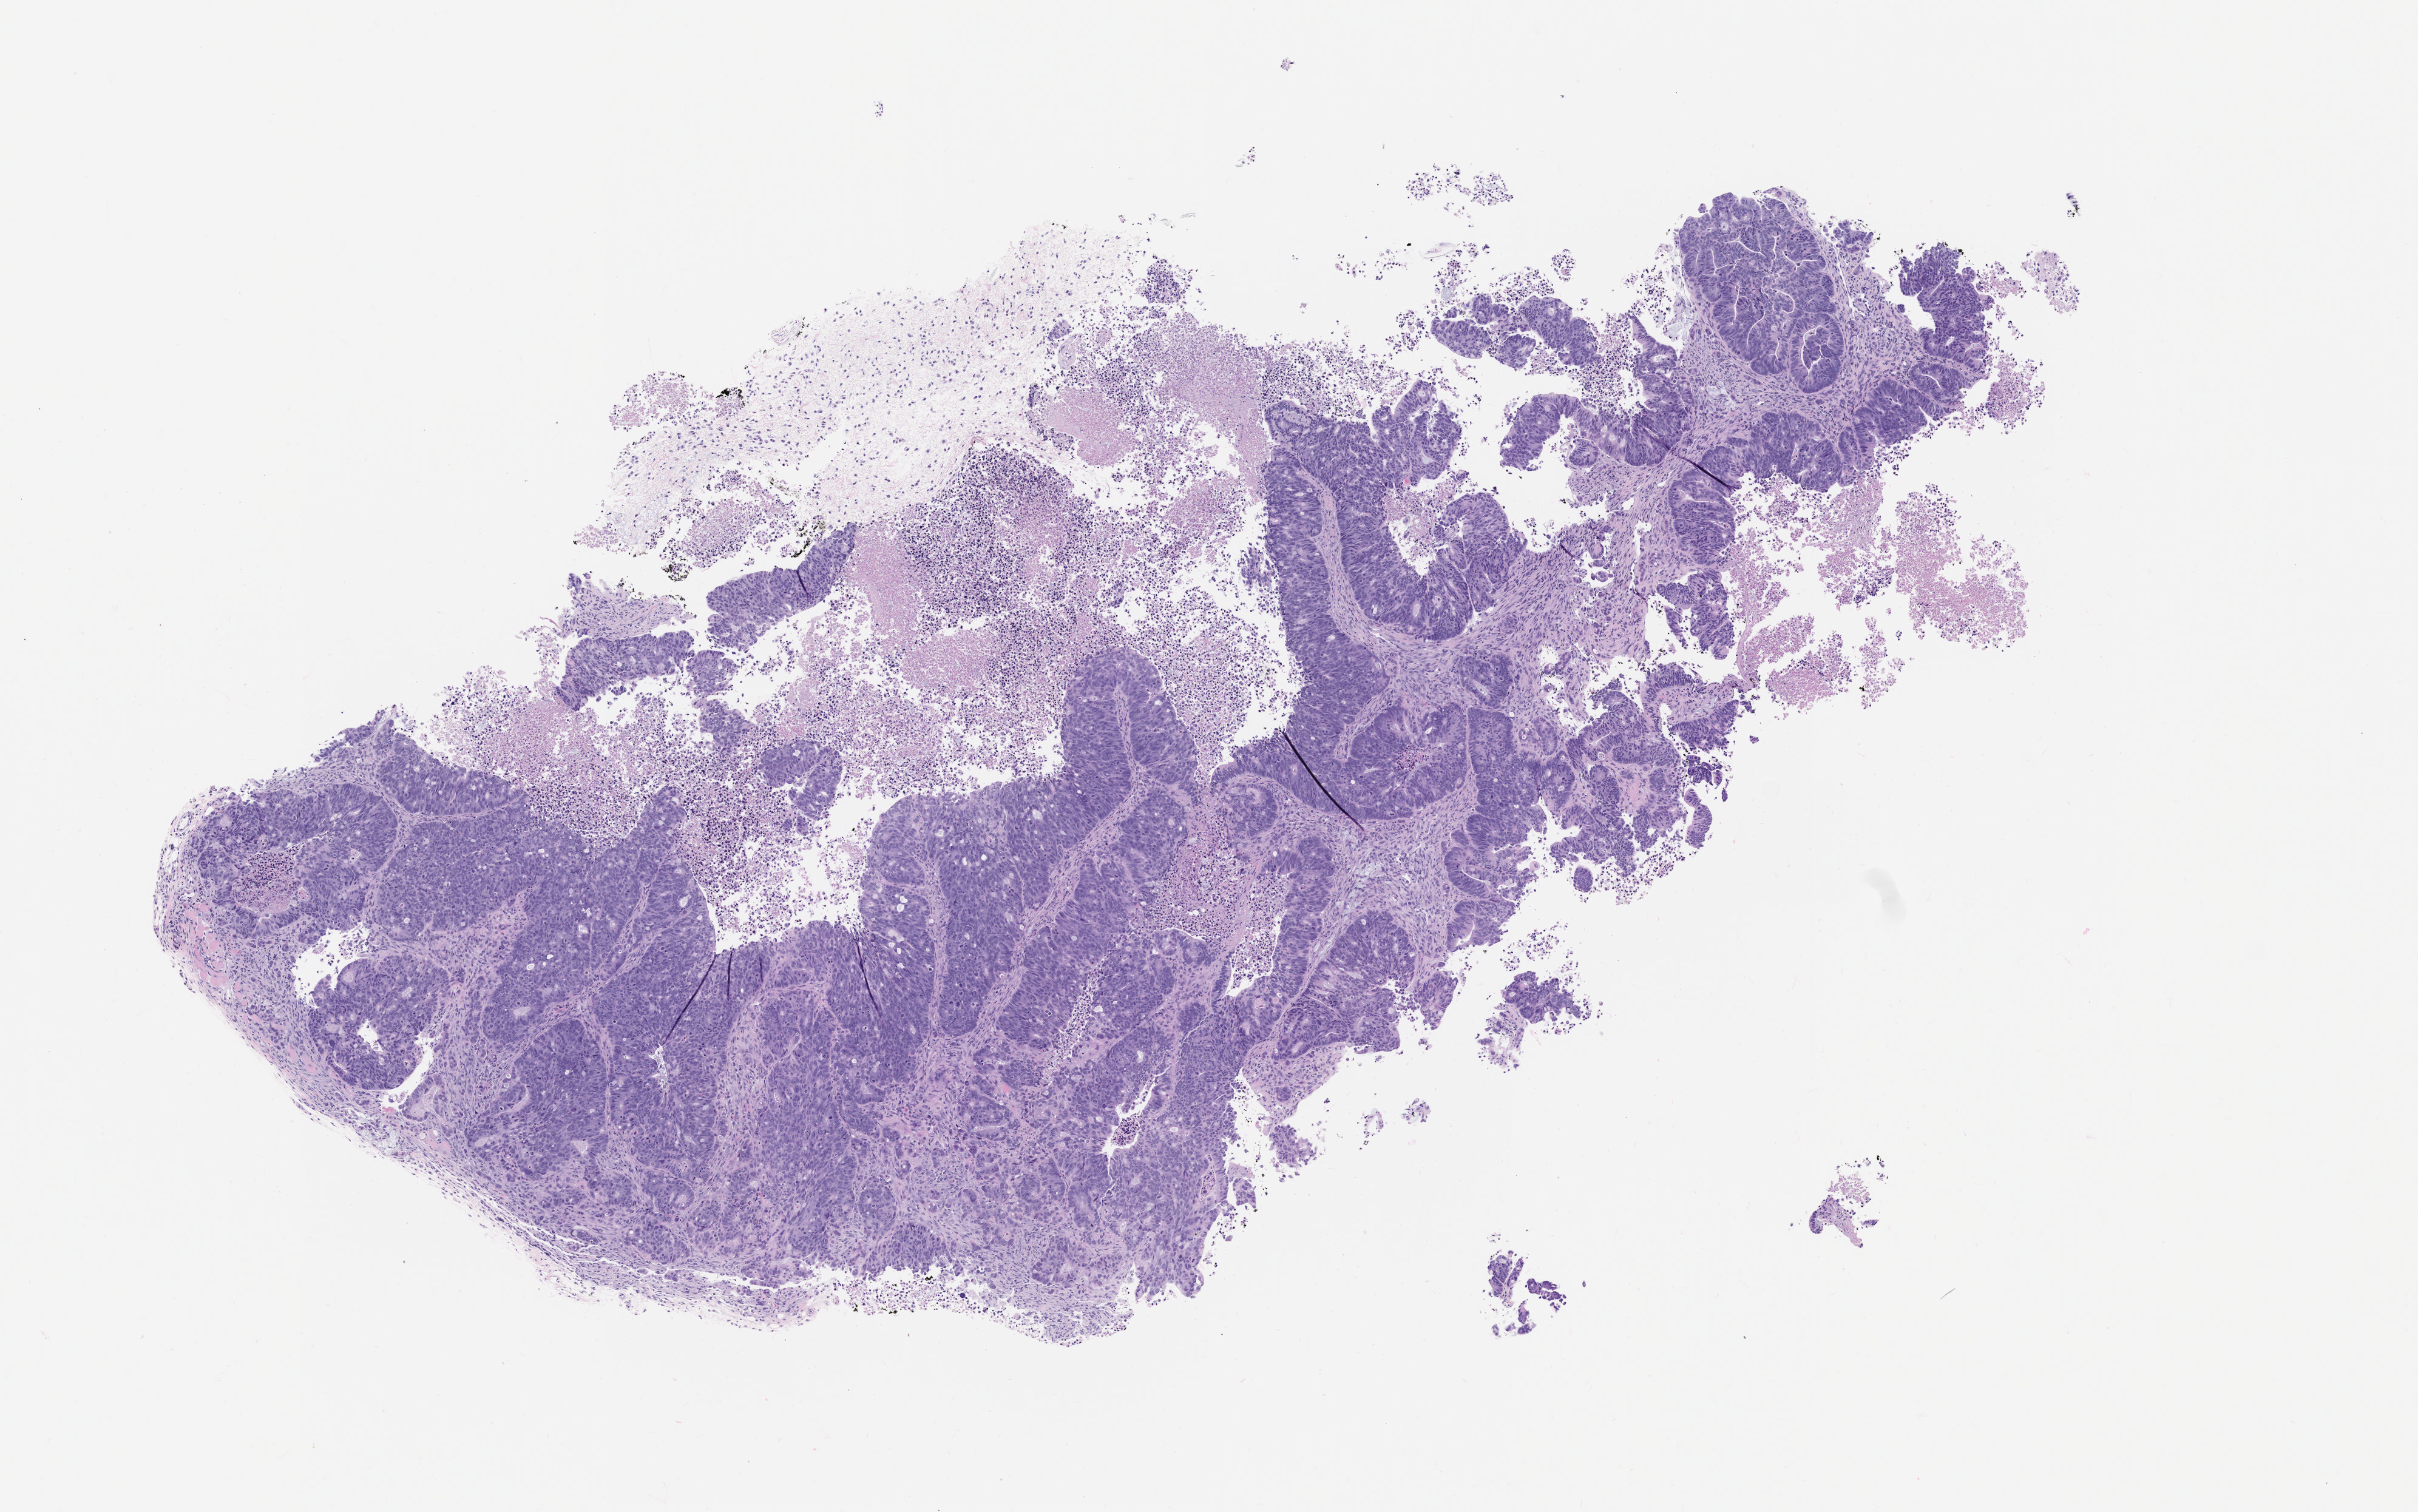
Whole-slide image, hematoxylin and eosin (H&E): patient-derived xenograft (human tumor grown in a mouse), passage 1 — low-resolution overview of the scanned area, about 8.0 x 5.0 mm; formalin-fixed paraffin-embedded section; tumor site category: colon.
Originating patient diagnosis: Colon Adenocarcinoma.